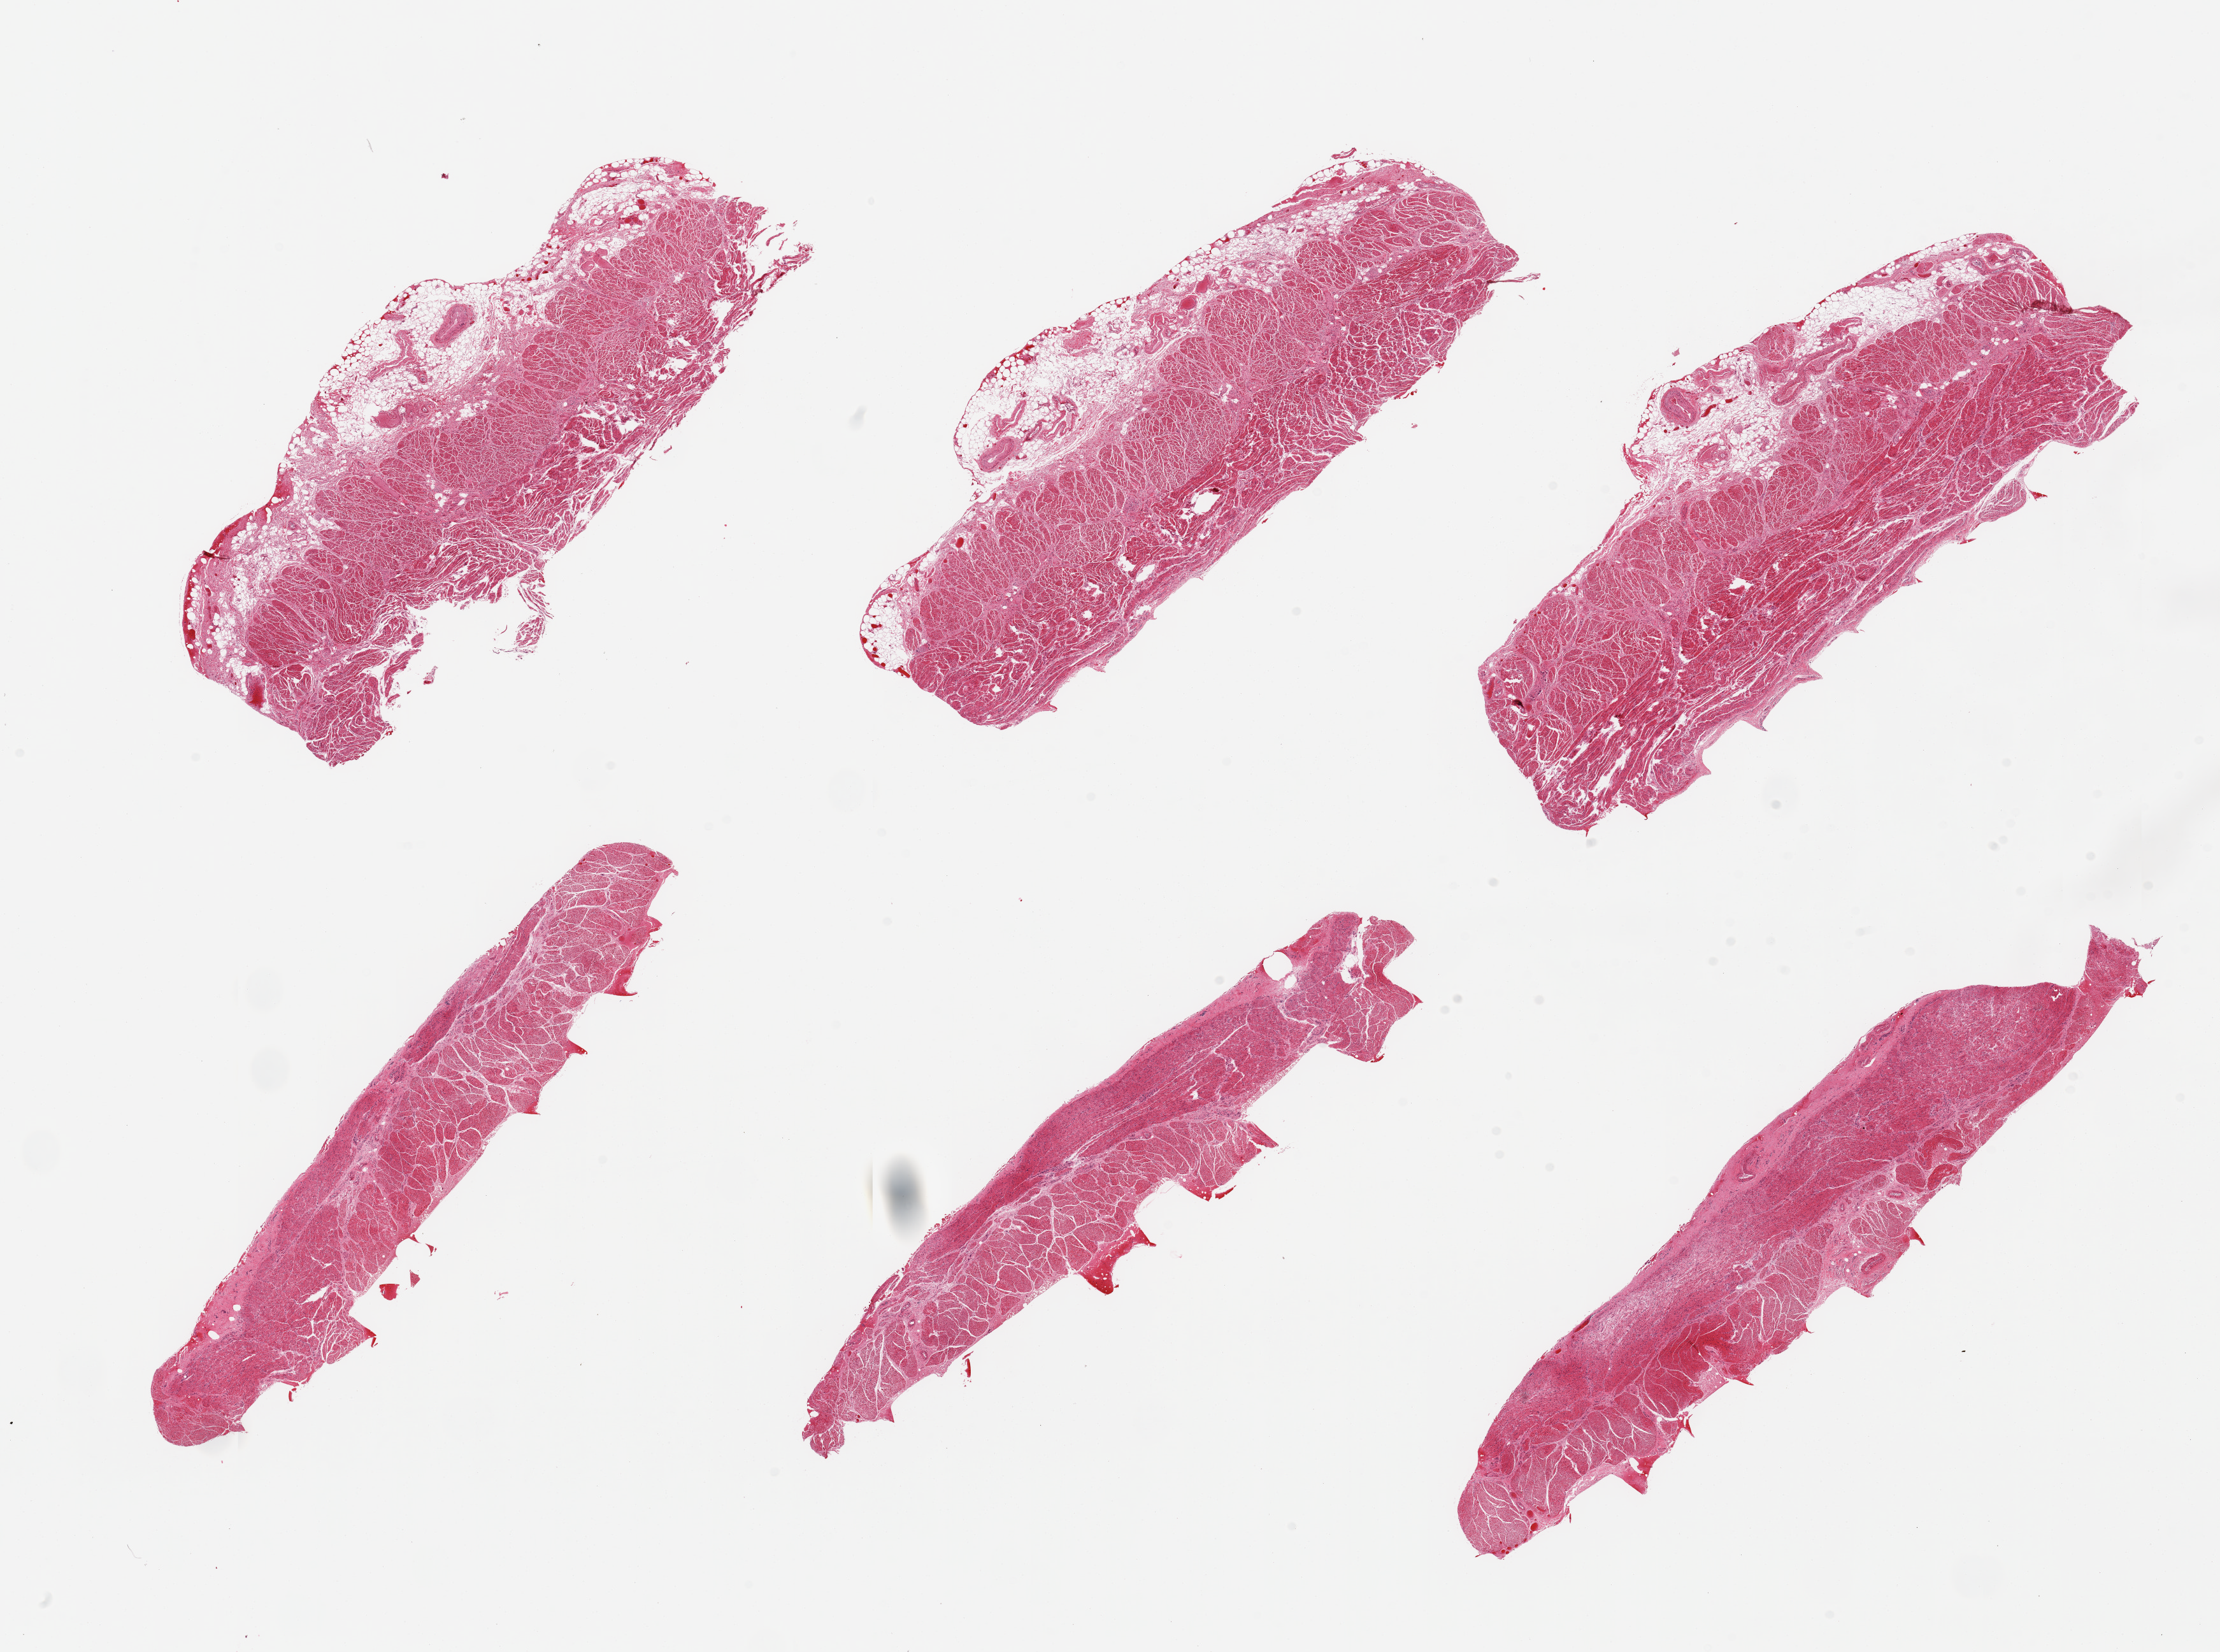
Haematoxylin and eosin whole-slide image, brightfield, low-resolution overview of the scanned area, about 27.6 x 20.5 mm (slide scanned at 20x), PAXgene-fixed paraffin-embedded (PFPE) section, target tissue: esophageal muscle, tissue donor sample. Donor sex: male.
• pathologist's review note for this sample: 6 pieces, ~0.5mm adherent rim of fat, several sections; otherwise all muscularis, good specimens